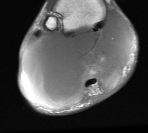
MRI of an extremity soft-tissue mass, one axial slice; slice 17 of 76 in the series (ordered by position); MR volume resampled by the dataset authors to the PET/CT grid (not the native acquisition matrix); 148 × 133 image matrix, field of view 145 × 130 mm. Male patient. Case-level facts recorded for this patient, not image findings: histological type: liposarcoma - round cell; grade: high; site of the primary tumour: right calf.
Structures marked on this image (expert contour drawn on MRI and transferred to this co-registered scan by the dataset authors):
- gross tumour volume (mass): box from (x=22, y=19) to (x=132, y=109) px